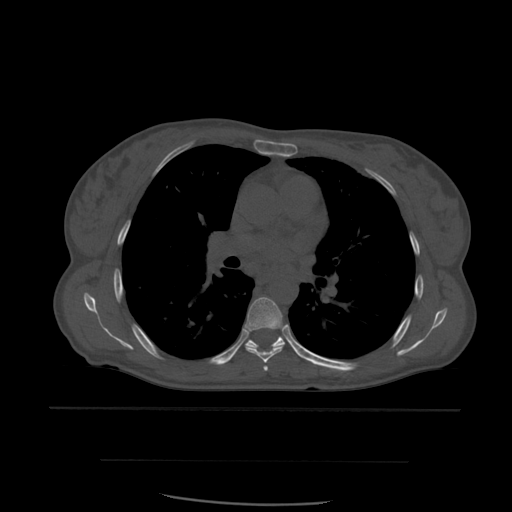
CT including the spine, one axial slice. Position 386 of 574 along the scan axis. Bone window (W 1800 / L 400 HU). 512 × 512 image matrix. Patient age 48 years. Case-level facts recorded for this patient, not image findings: primary cancer: lung; vertebrae with lytic lesions (as recorded): T11.
Structures marked on this image (semi-automatically segmented with operator editing):
- T5 vertebra: bounding box [x1, y1, x2, y2] px = [263, 366, 269, 372]
- T6 vertebra: [245, 297, 287, 363]
- T7 vertebra: [229, 329, 304, 361]